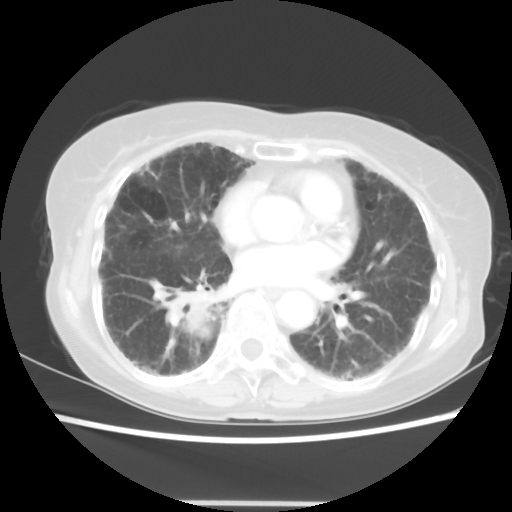
Chest CT, one axial slice. Position 24 of 52 along the scan axis. Reconstruction kernel STANDARD. 120 kVp. Lung window (W 1500 / L -600 HU). 5 mm slice thickness. 512 × 512 image matrix. Patient: female, 71 years. Case-level facts recorded for this patient, not image findings: clinical TNM (as recorded): T3 N0 M0.
Structures marked on this image (rectangle marked by the reading radiologist):
- lung tumour (recorded histology: squamous cell carcinoma): bounding box <165,292,219,346> (left, top, right, bottom; pixels)